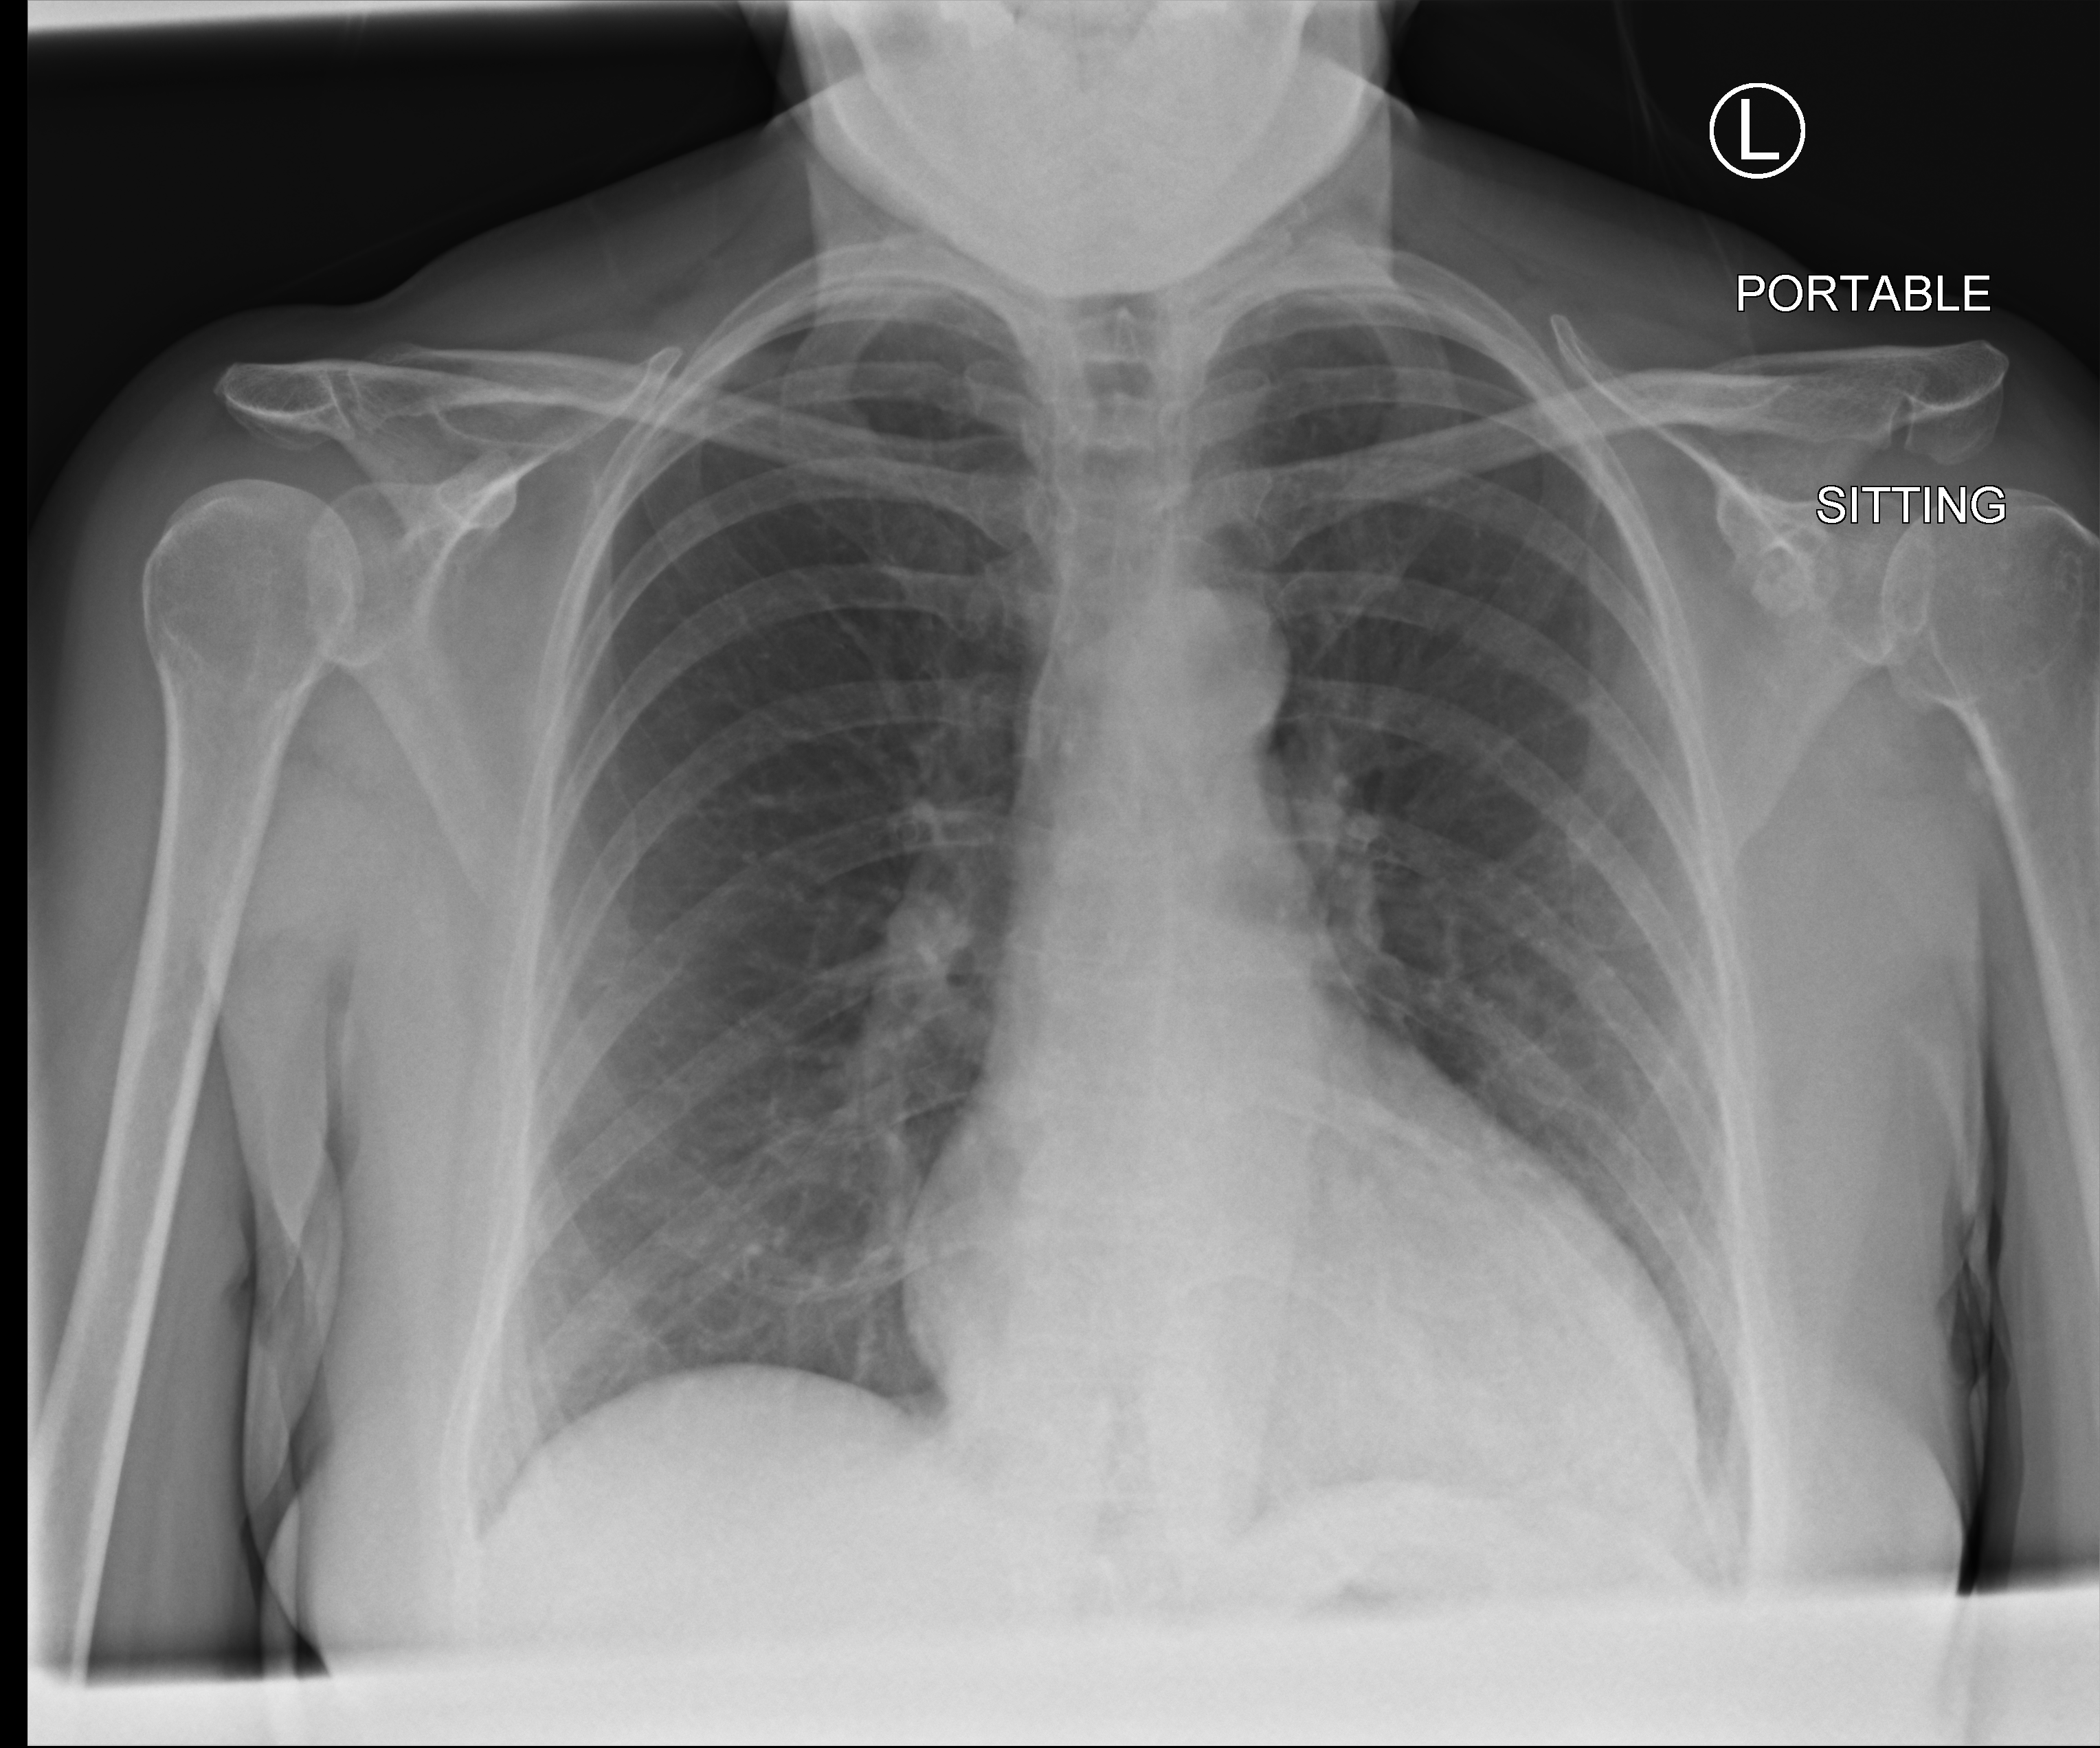
Bedside chest radiograph (computed radiography), anteroposterior (AP) projection. Female patient hospitalised with COVID-19, age 60–74 years.
Admission-level facts for this patient (not findings on this image; timing relative to this image not recorded): COPD (admission record): no; admitted to intensive care during this hospital stay: no.